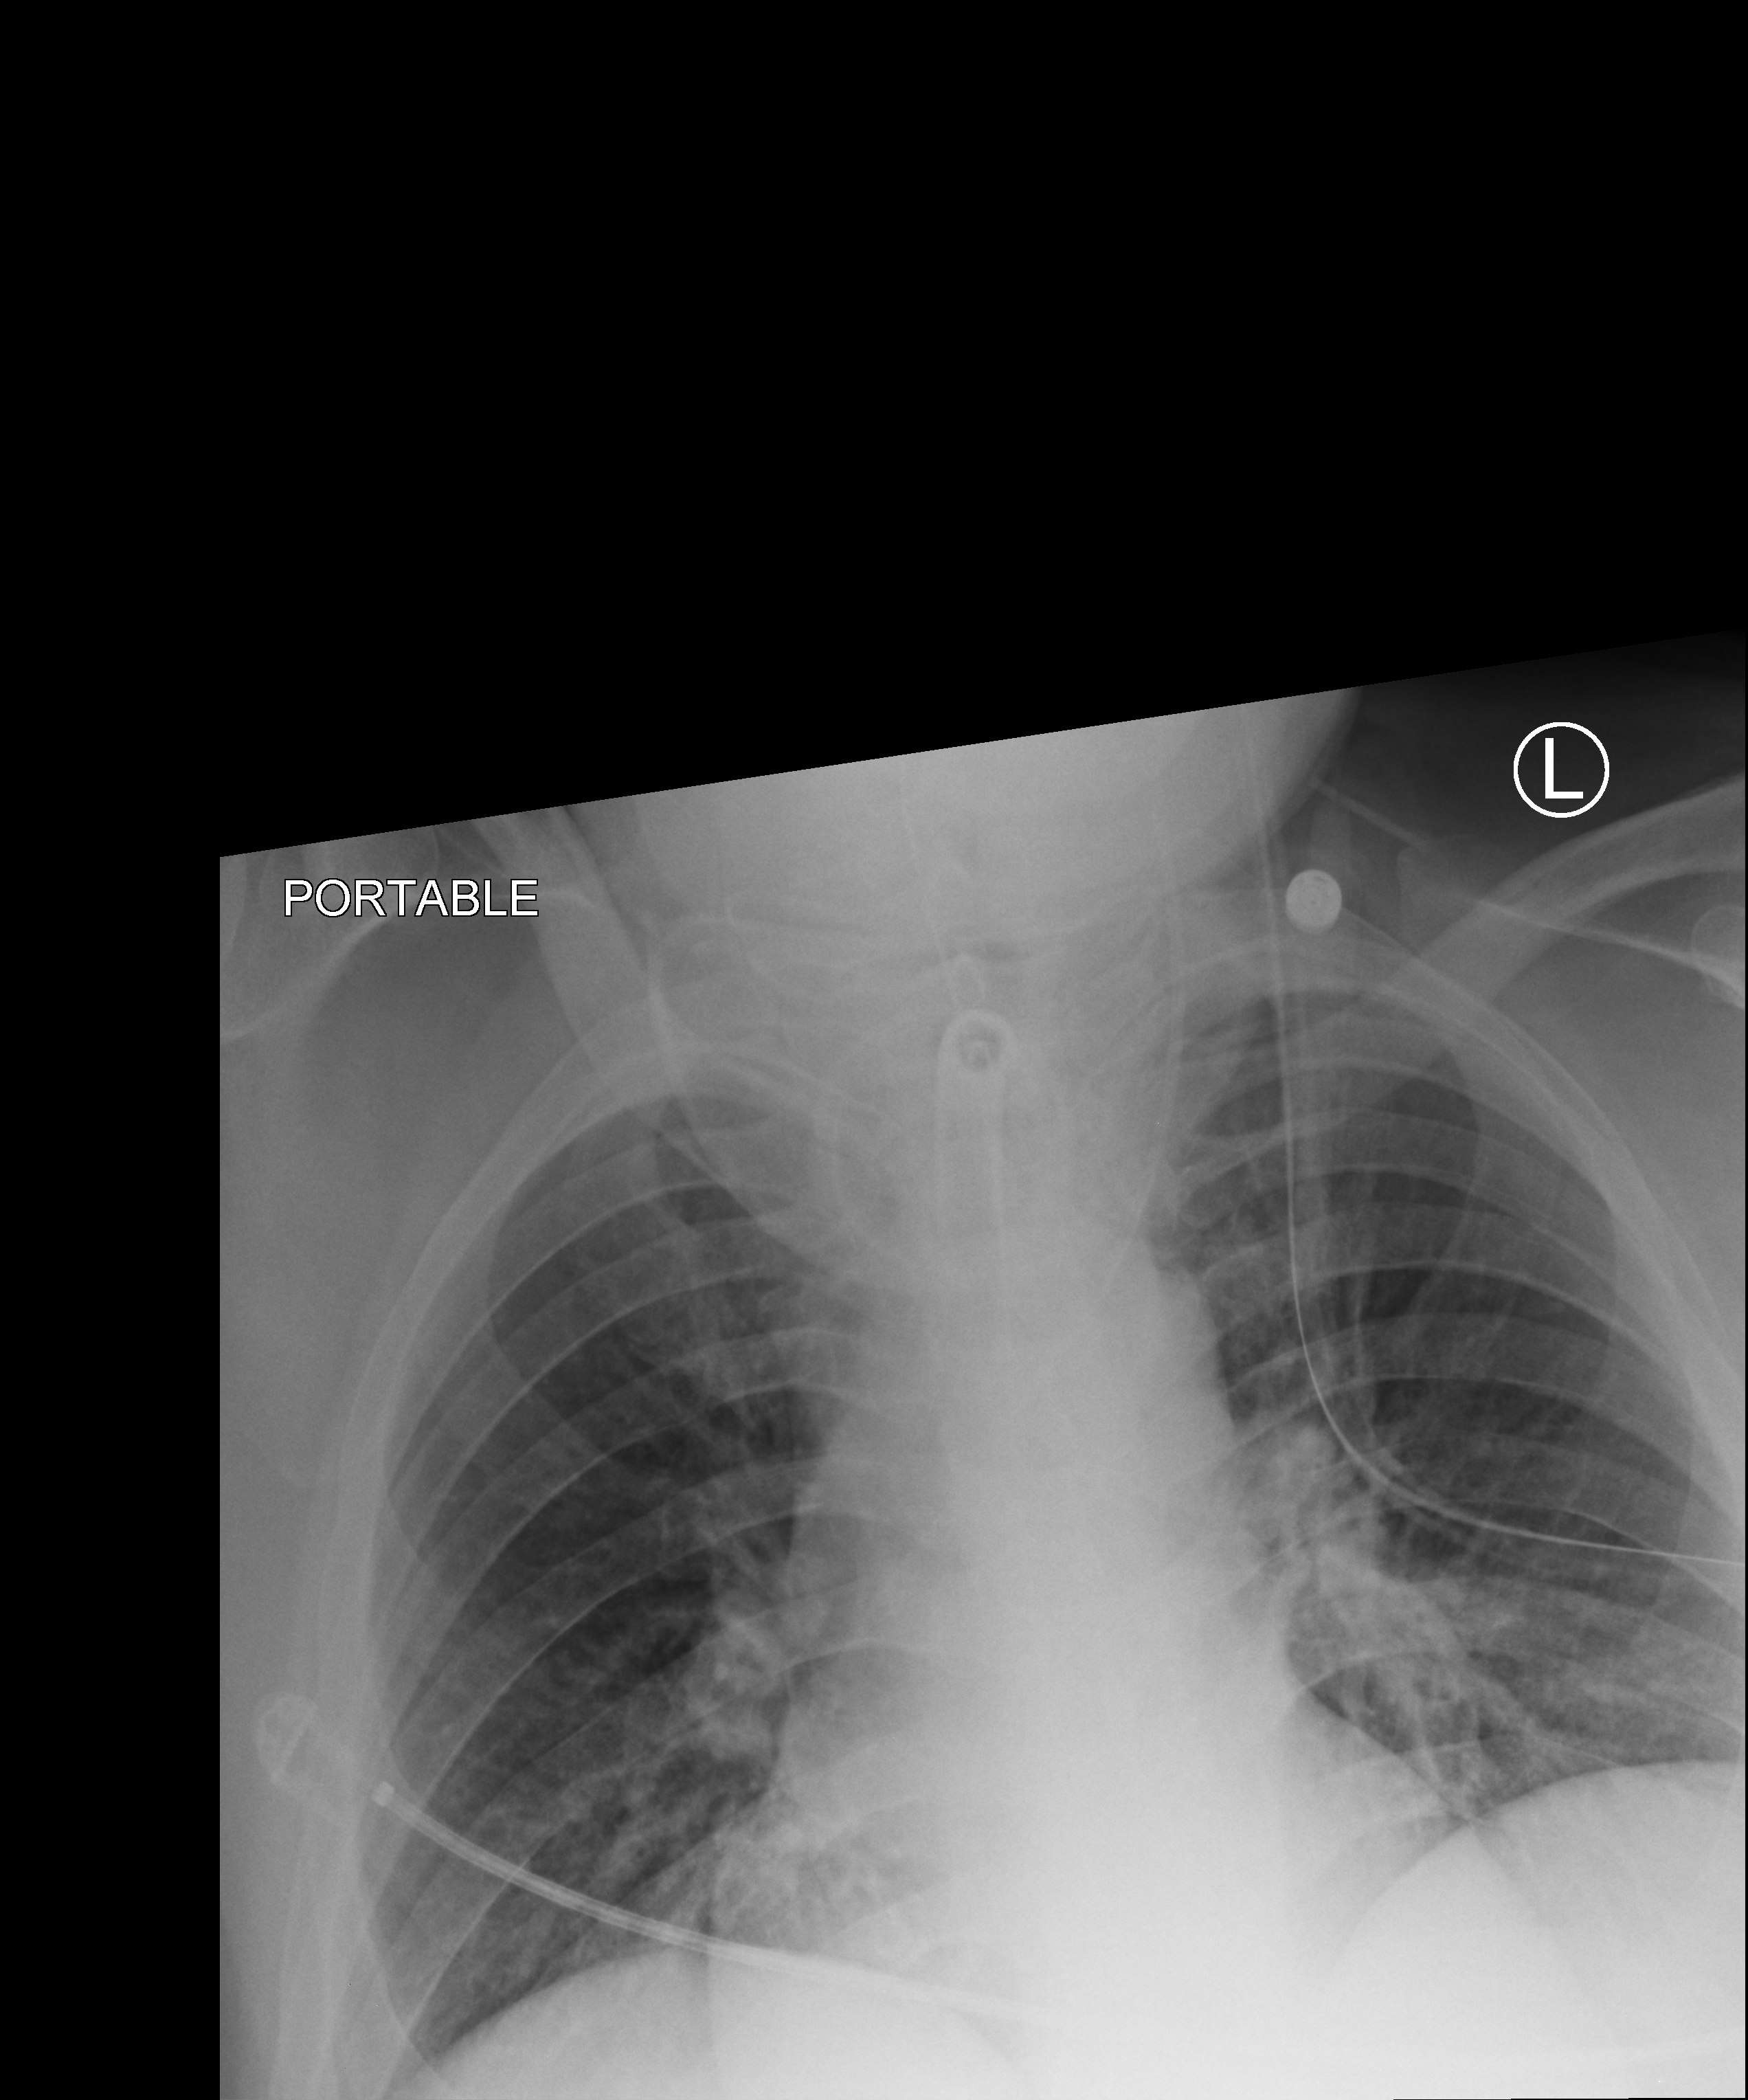
Portable chest radiograph; anteroposterior (AP) projection. Patient hospitalised with COVID-19; male, aged 18–59 years.
From the hospital-stay record, not from the radiograph (when in the stay this image was taken is not recorded): mechanically ventilated during this hospital stay: yes; length of hospital stay: 65 days; admitted to intensive care during this hospital stay: yes.